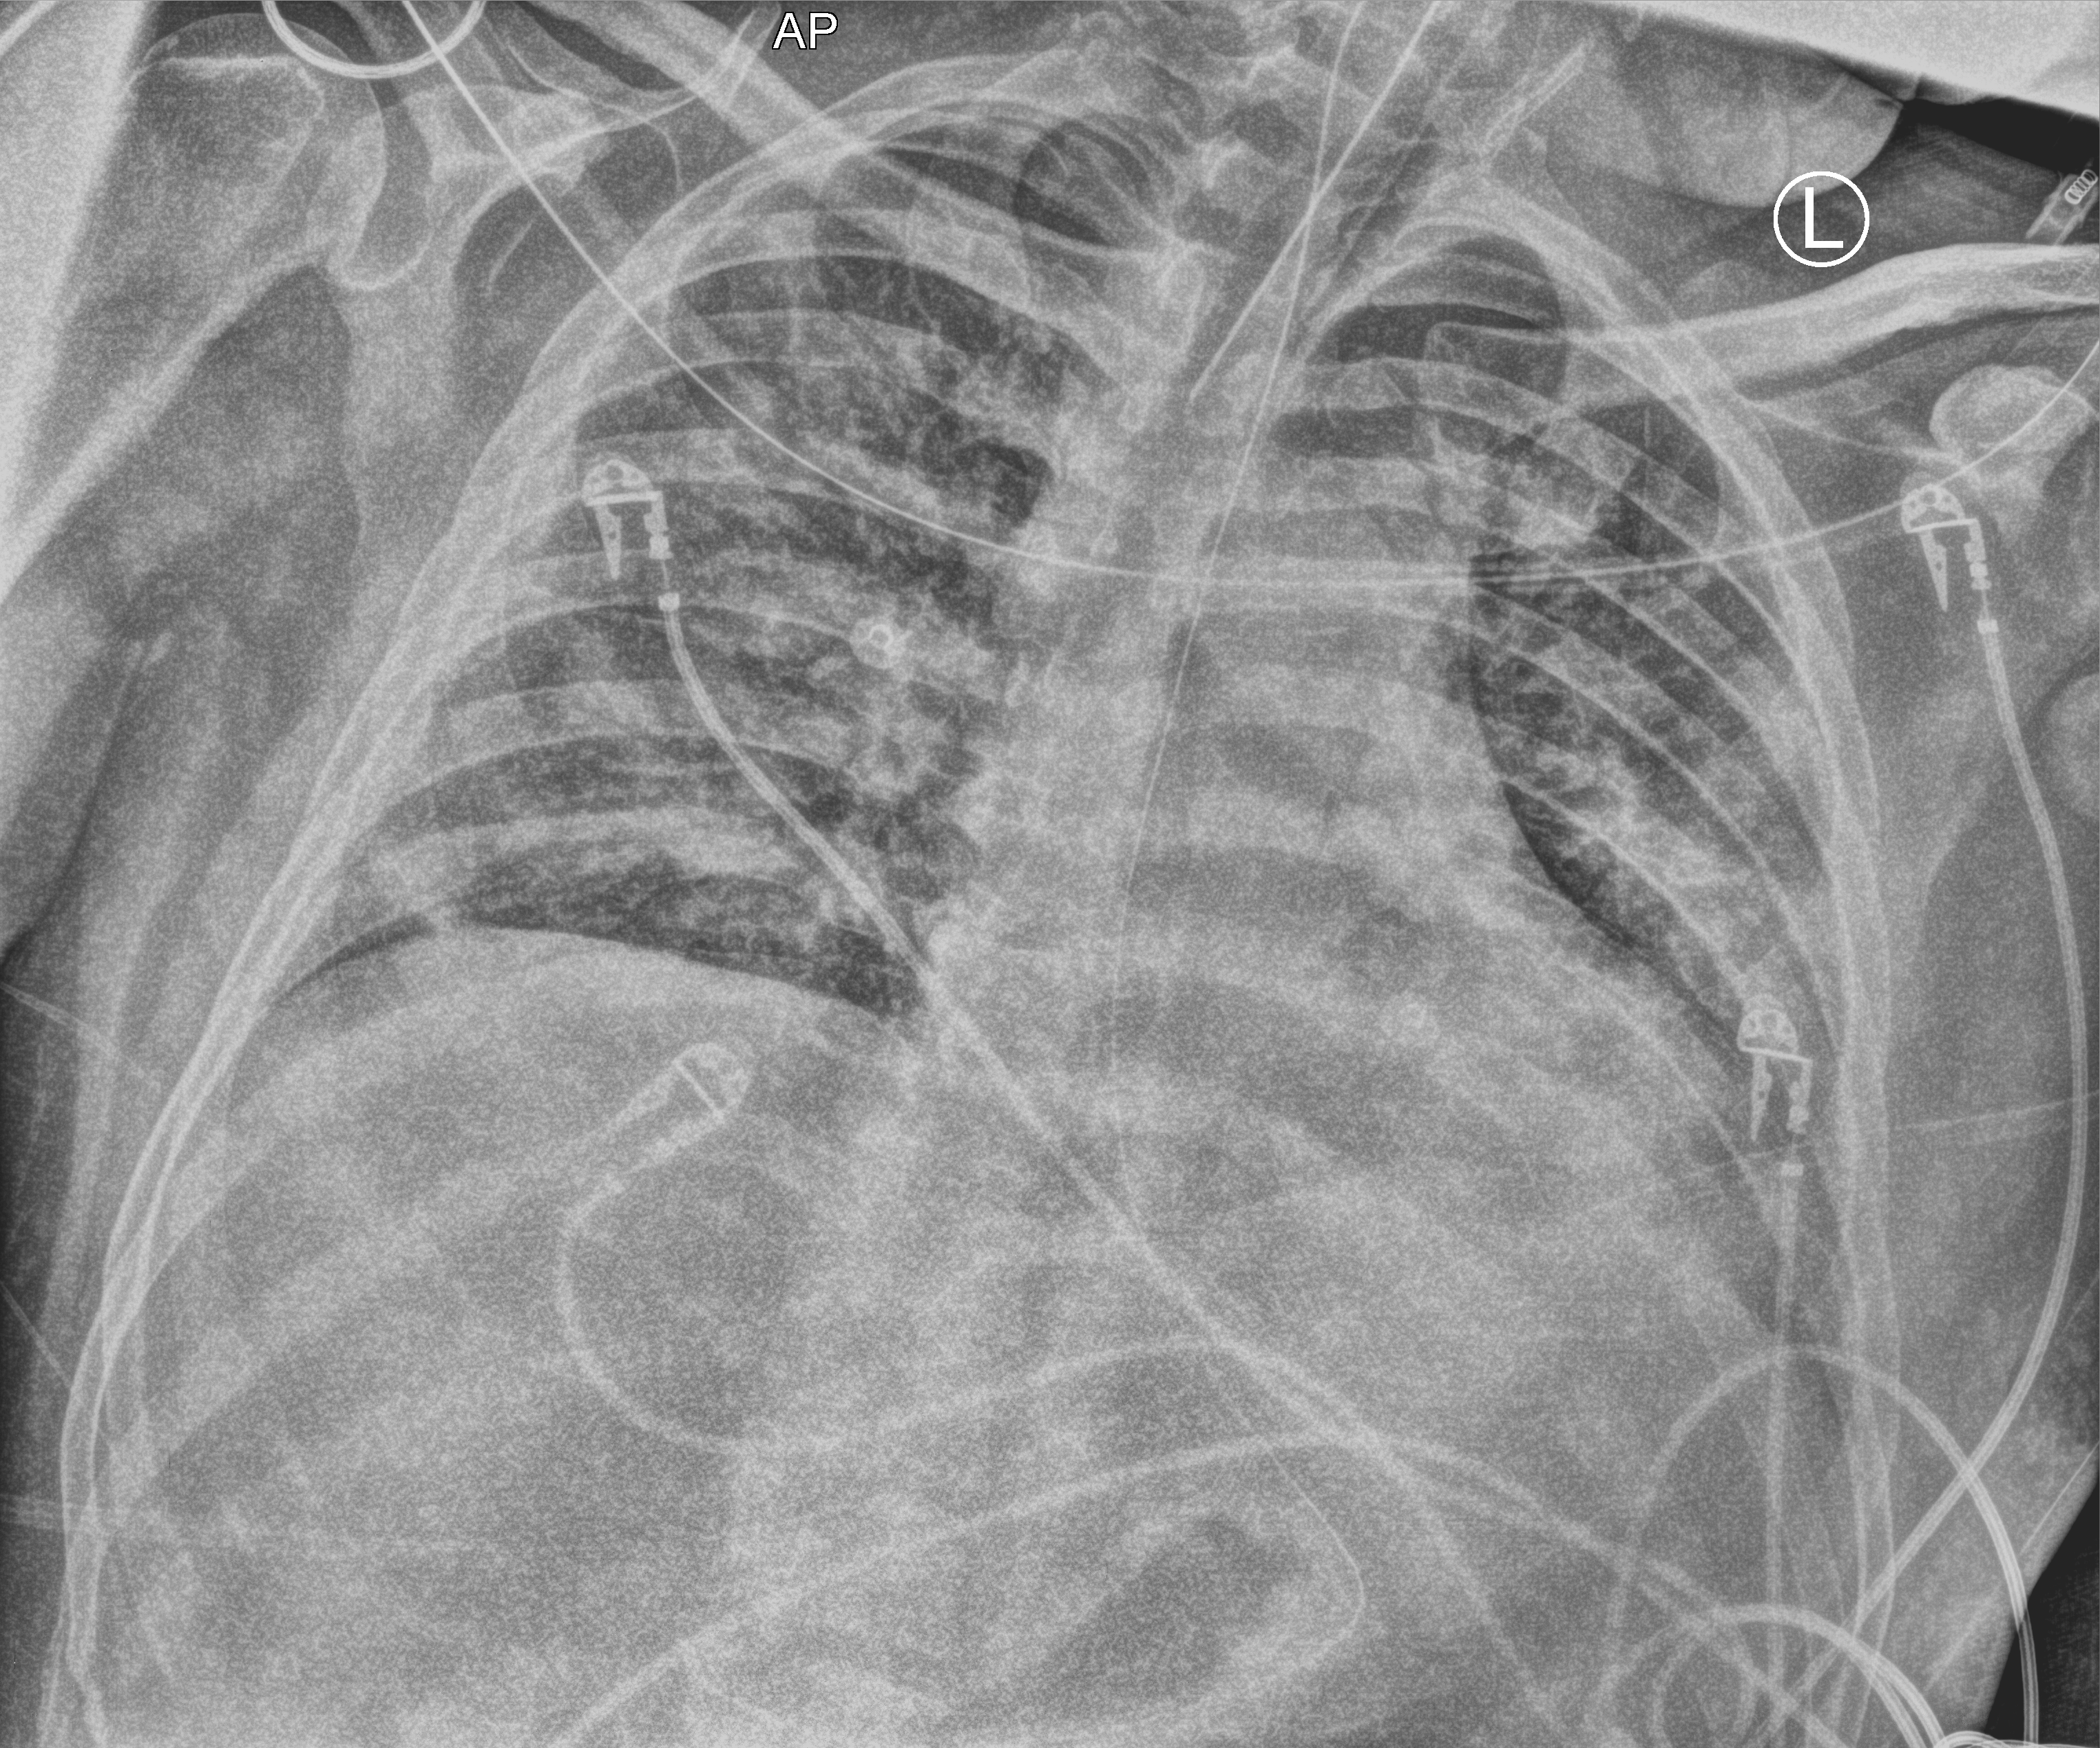
Chest X-ray (portable); anteroposterior (AP) projection. Male patient hospitalised with COVID-19, age 18–59 years.
From the hospital-stay record, not from the radiograph (when in the stay this image was taken is not recorded): mechanically ventilated during this hospital stay: yes; chronic kidney disease (admission record): no; hypertension (admission record): yes.